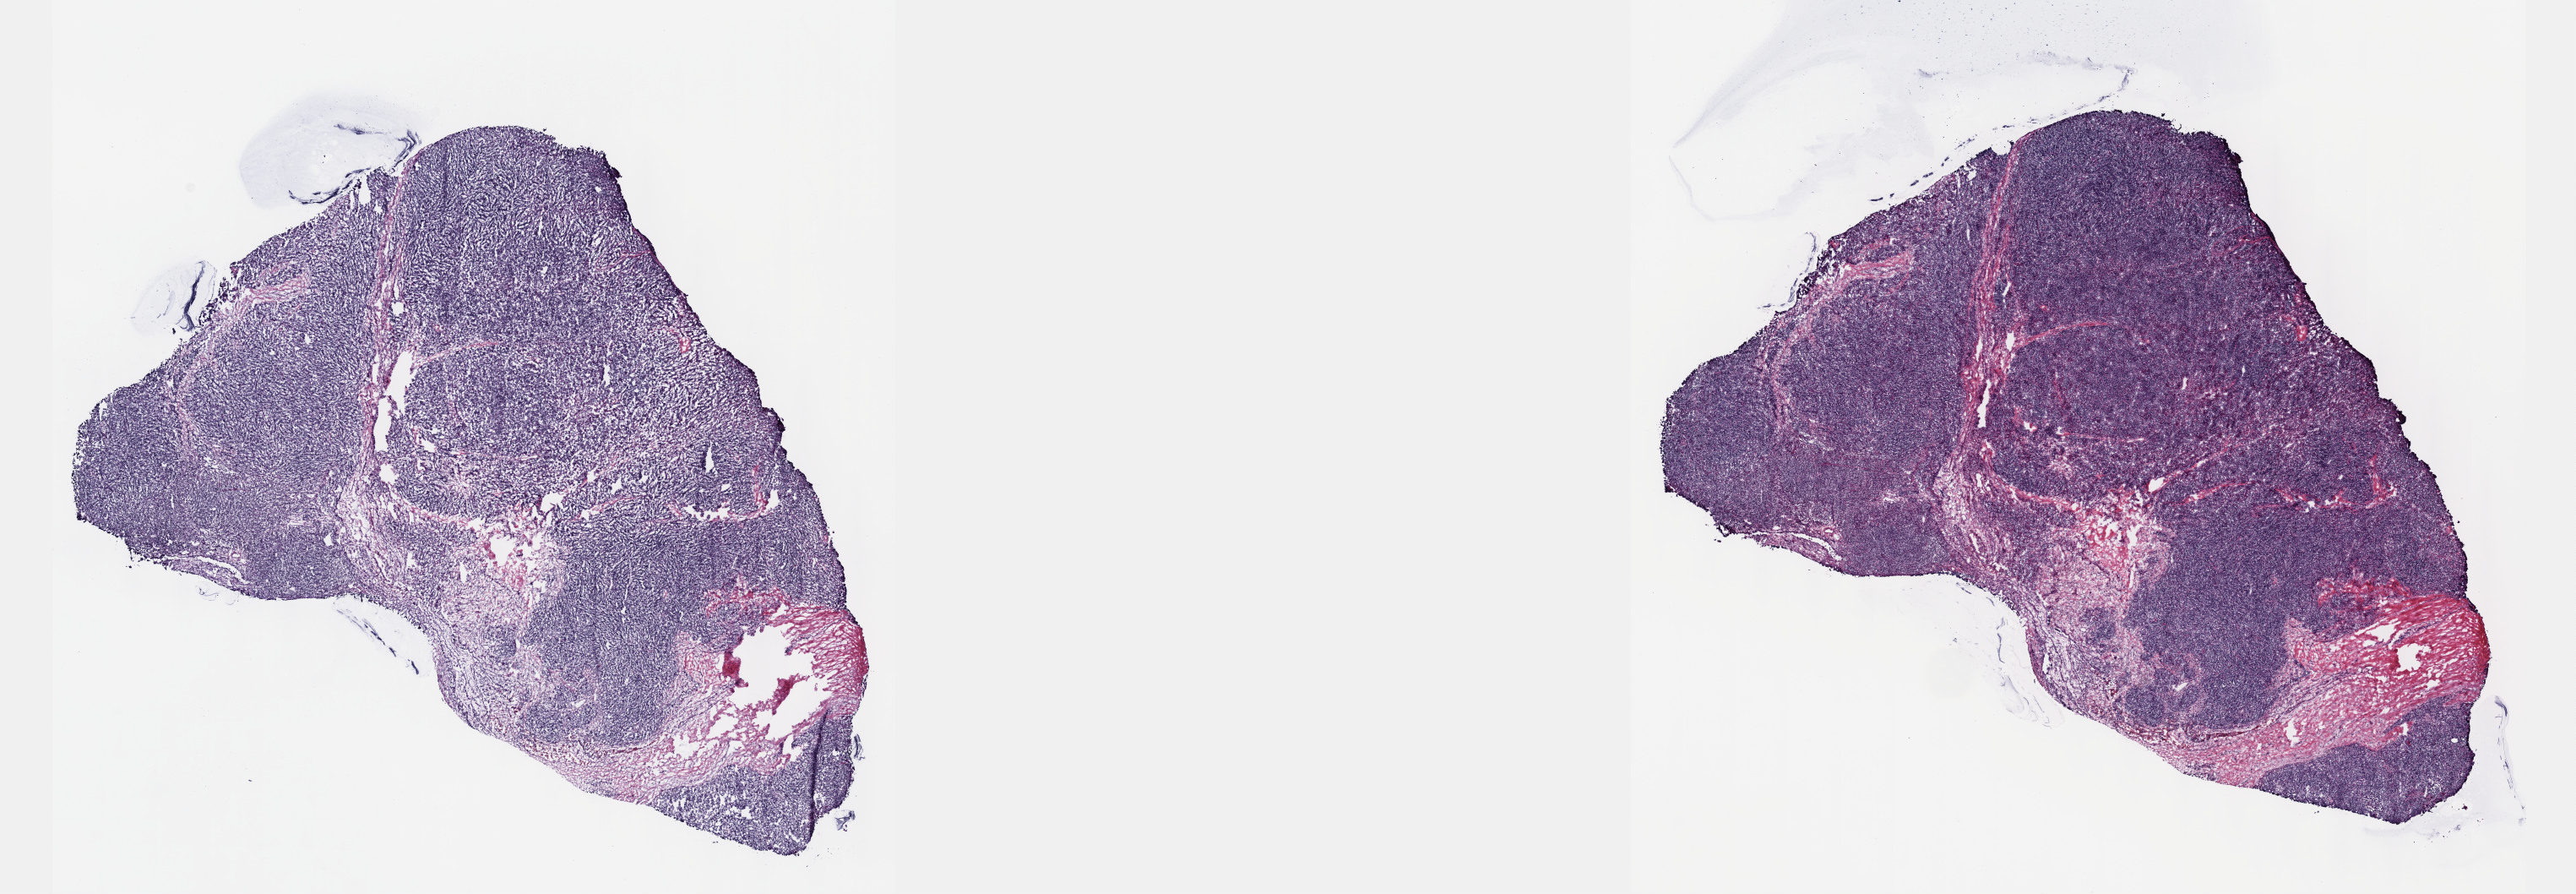
Hematoxylin and eosin (H&E) stained whole-slide image, shown as a low-resolution overview of the whole scanned area (about 24.6 x 8.5 mm, slide scanned at 40x), frozen section from the top of the tissue portion, thymus, primary tumour sample. Patient: male, age at initial diagnosis 43 years.
Pathologic diagnosis: Thymoma, type B2, malignant.